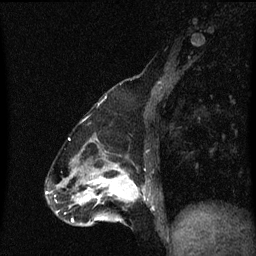
Breast MRI (dynamic contrast-enhanced), one sagittal slice. Slice 23 of 60 in the series (ordered by position). Dynamic contrast-enhanced series, image 2 of 3 at this slice position (ordered by acquisition). 1.5 T. TE 4.2 ms, TR 8.4 ms. 256 × 256 image matrix, field of view 200 × 200 mm. Female patient, age 47 years.
Outlined on this slice (semi-automatic segmentation, software-assisted and operator-edited):
- analysis volume of interest (the breast-tissue region the enhancement analysis was run in; not a lesion): bounding box (x1, y1, x2, y2) in pixels: (100, 172, 151, 219)
- tumour enhancement mask (voxels above the 70 % enhancement threshold inside the analysis volume of interest): (100, 172, 146, 201)